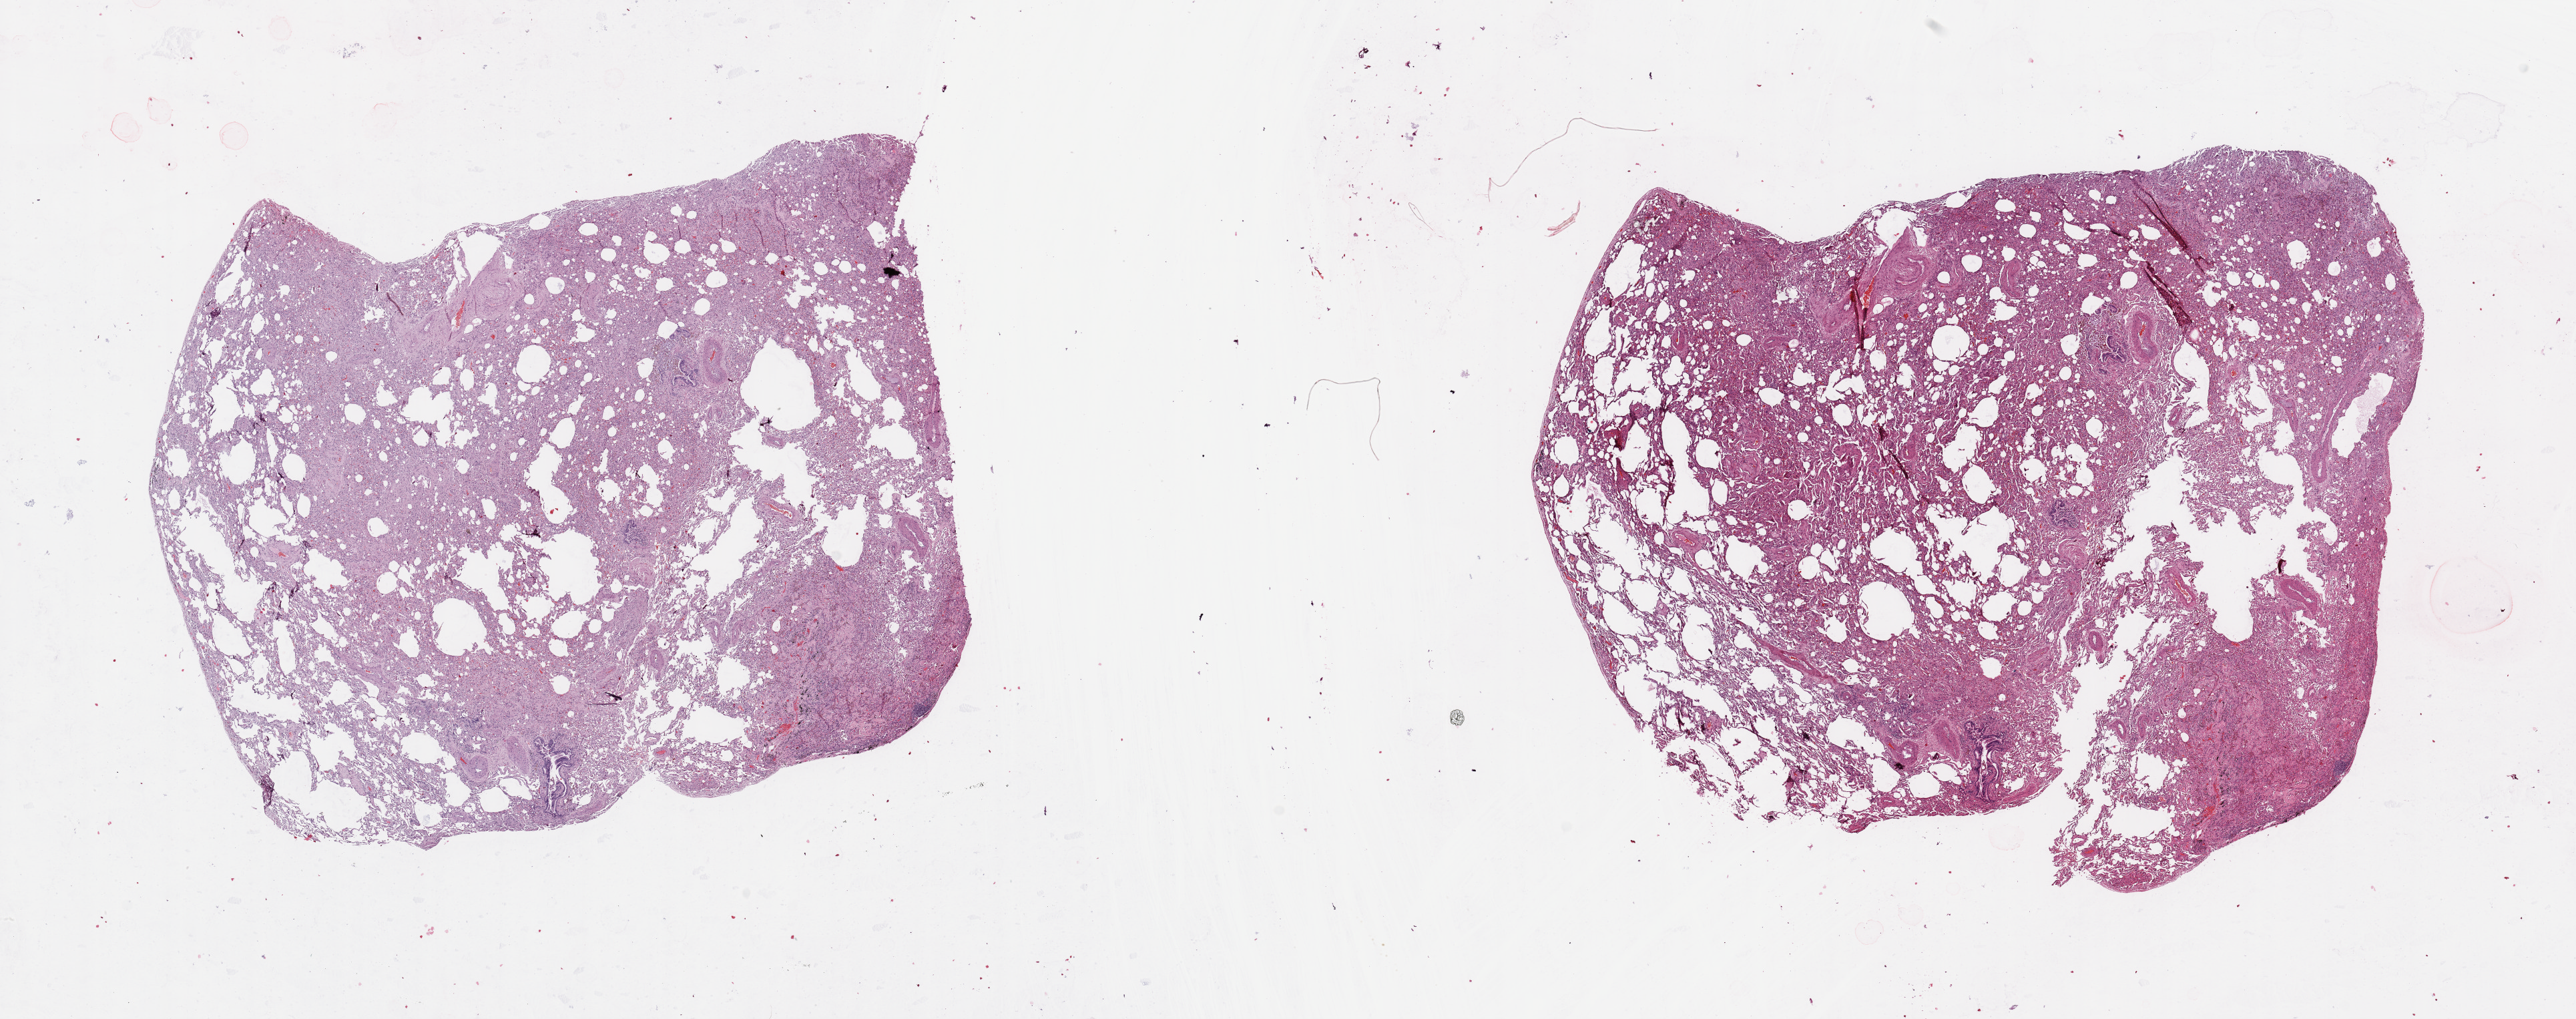
Digitized H&E-stained tissue section (whole slide) — shown as a low-resolution overview of the whole scanned area (about 30.5 x 12.1 mm, from a 20x scan). Lung, normal (non-tumour) tissue. Patient: female, age 64 years.
This section: normal (non-tumour) tissue from the same patient. Patient diagnosis: Squamous cell carcinoma, NOS.